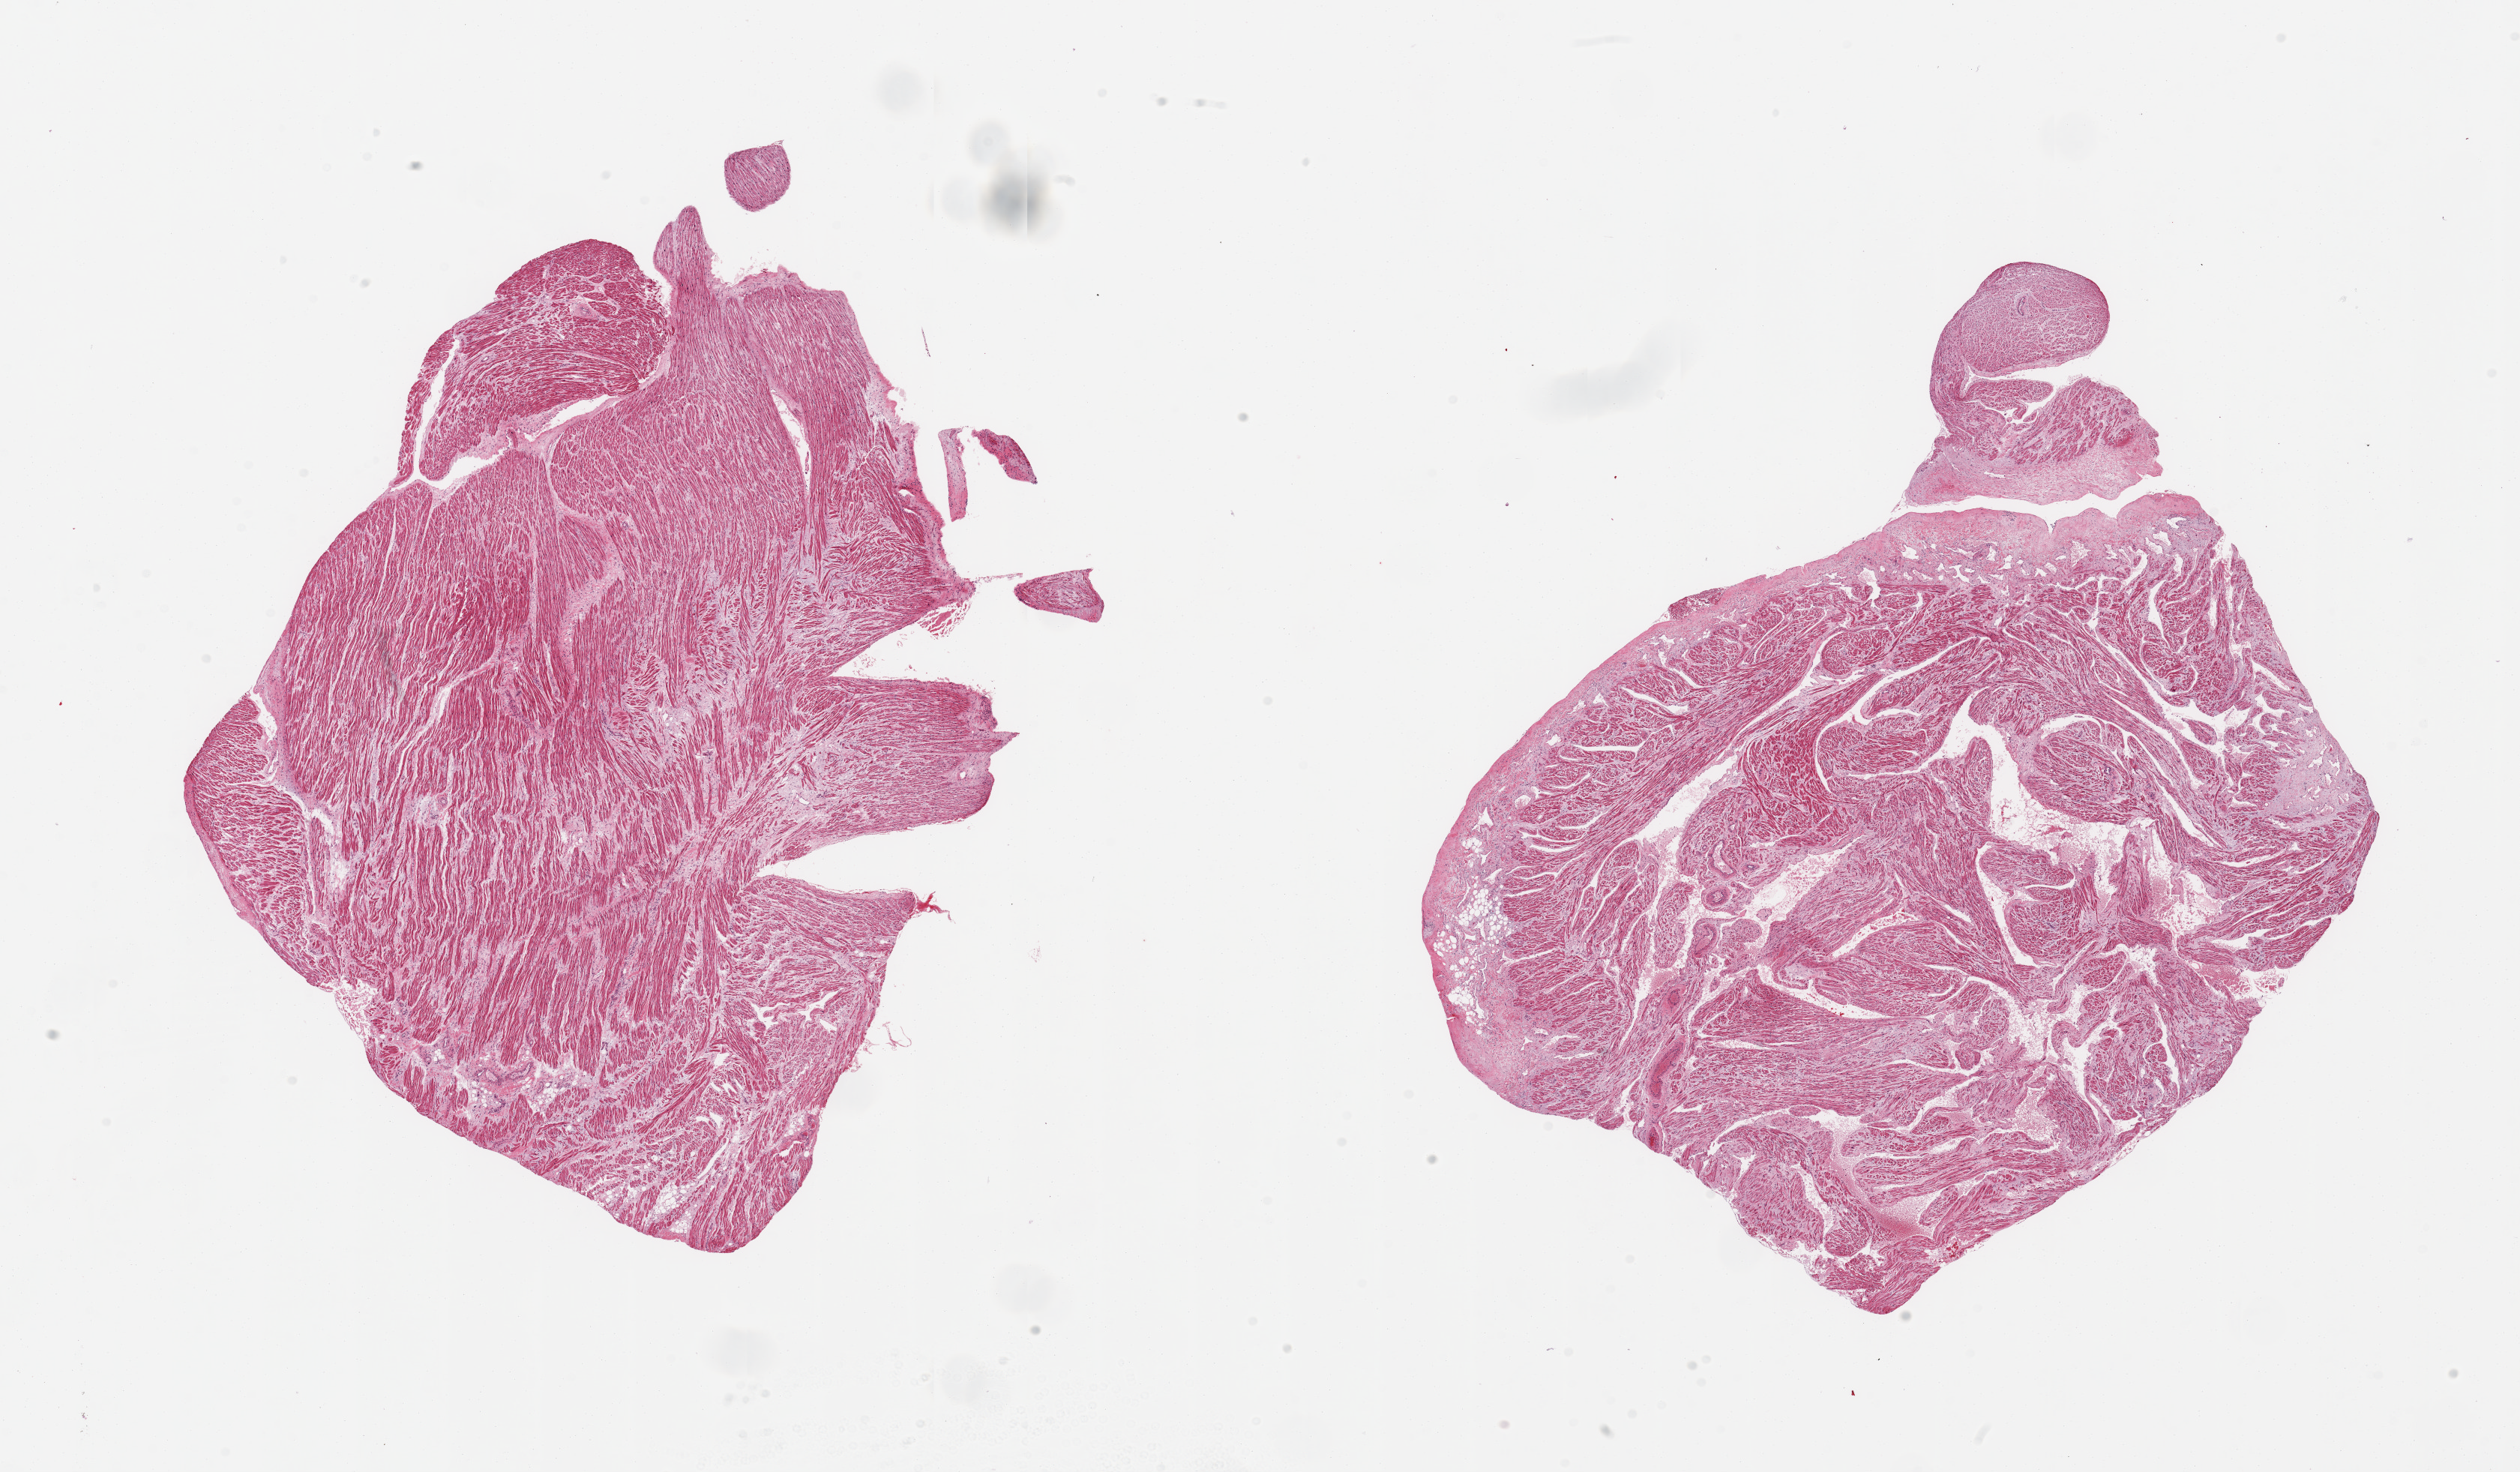
H&E whole-slide image, brightfield — shown as a low-resolution overview of the whole scanned area (about 26.6 x 15.5 mm). PAXgene-fixed, paraffin-embedded tissue. Section of auricular appendage (target tissue). Tissue donor sample. Donor sex: female.
Pathologist's review note for this sample: 2 pieces, no abnormalities.